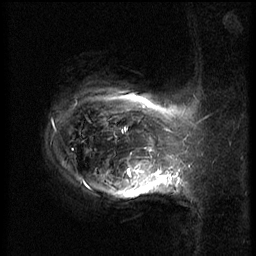
Breast MRI (dynamic contrast-enhanced), one sagittal slice; position 52 of 62 along the scan axis; 3 images stored at this slice position (order not interpretable as contrast timing); 1.5 T; TE 4.2 ms, TR 8.9 ms; 2.5 mm slice thickness; 256 × 256 image matrix, field of view 200 × 200 mm. Female patient, age 37 years. Case-level facts recorded for this patient, not image findings: setting: breast cancer imaged before/during neoadjuvant chemotherapy; receptor status: triple-negative.
Structures marked on this image (semi-automatically segmented with operator editing):
- analysis volume of interest (the breast-tissue region the enhancement analysis was run in; not a lesion): bounding box (x1, y1, x2, y2) in pixels: (116, 146, 168, 203)
- tumour enhancement mask (voxels above the 140 % enhancement threshold inside the analysis volume of interest): (128, 169, 130, 175)